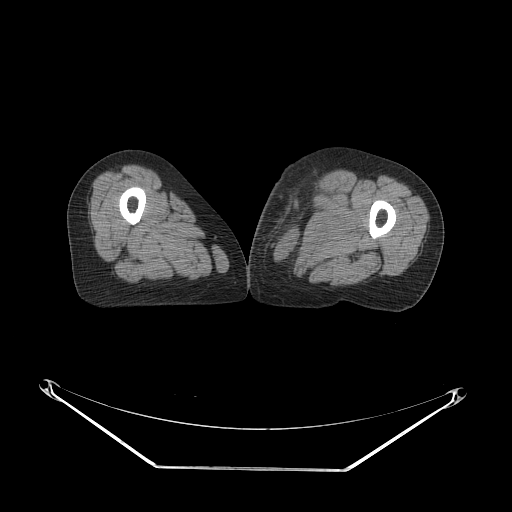
CT of an extremity soft-tissue mass (from a PET/CT study), one axial slice. Position 48 of 91 along the scan axis. 140 kVp. Soft-tissue window (W 400 / L 40 HU). 3.75 mm slice thickness. 512 × 512 image matrix. Female patient. Case-level facts recorded for this patient, not image findings: histological type: pleomorphic leiomyosarcoma; grade: high; site of the primary tumour: left thigh.
Annotated regions visible in this slice (expert contour drawn on MRI and transferred to this co-registered scan by the dataset authors):
- gross tumour volume including surrounding oedema: bounding box (x1, y1, x2, y2) in pixels: (263, 171, 327, 238)